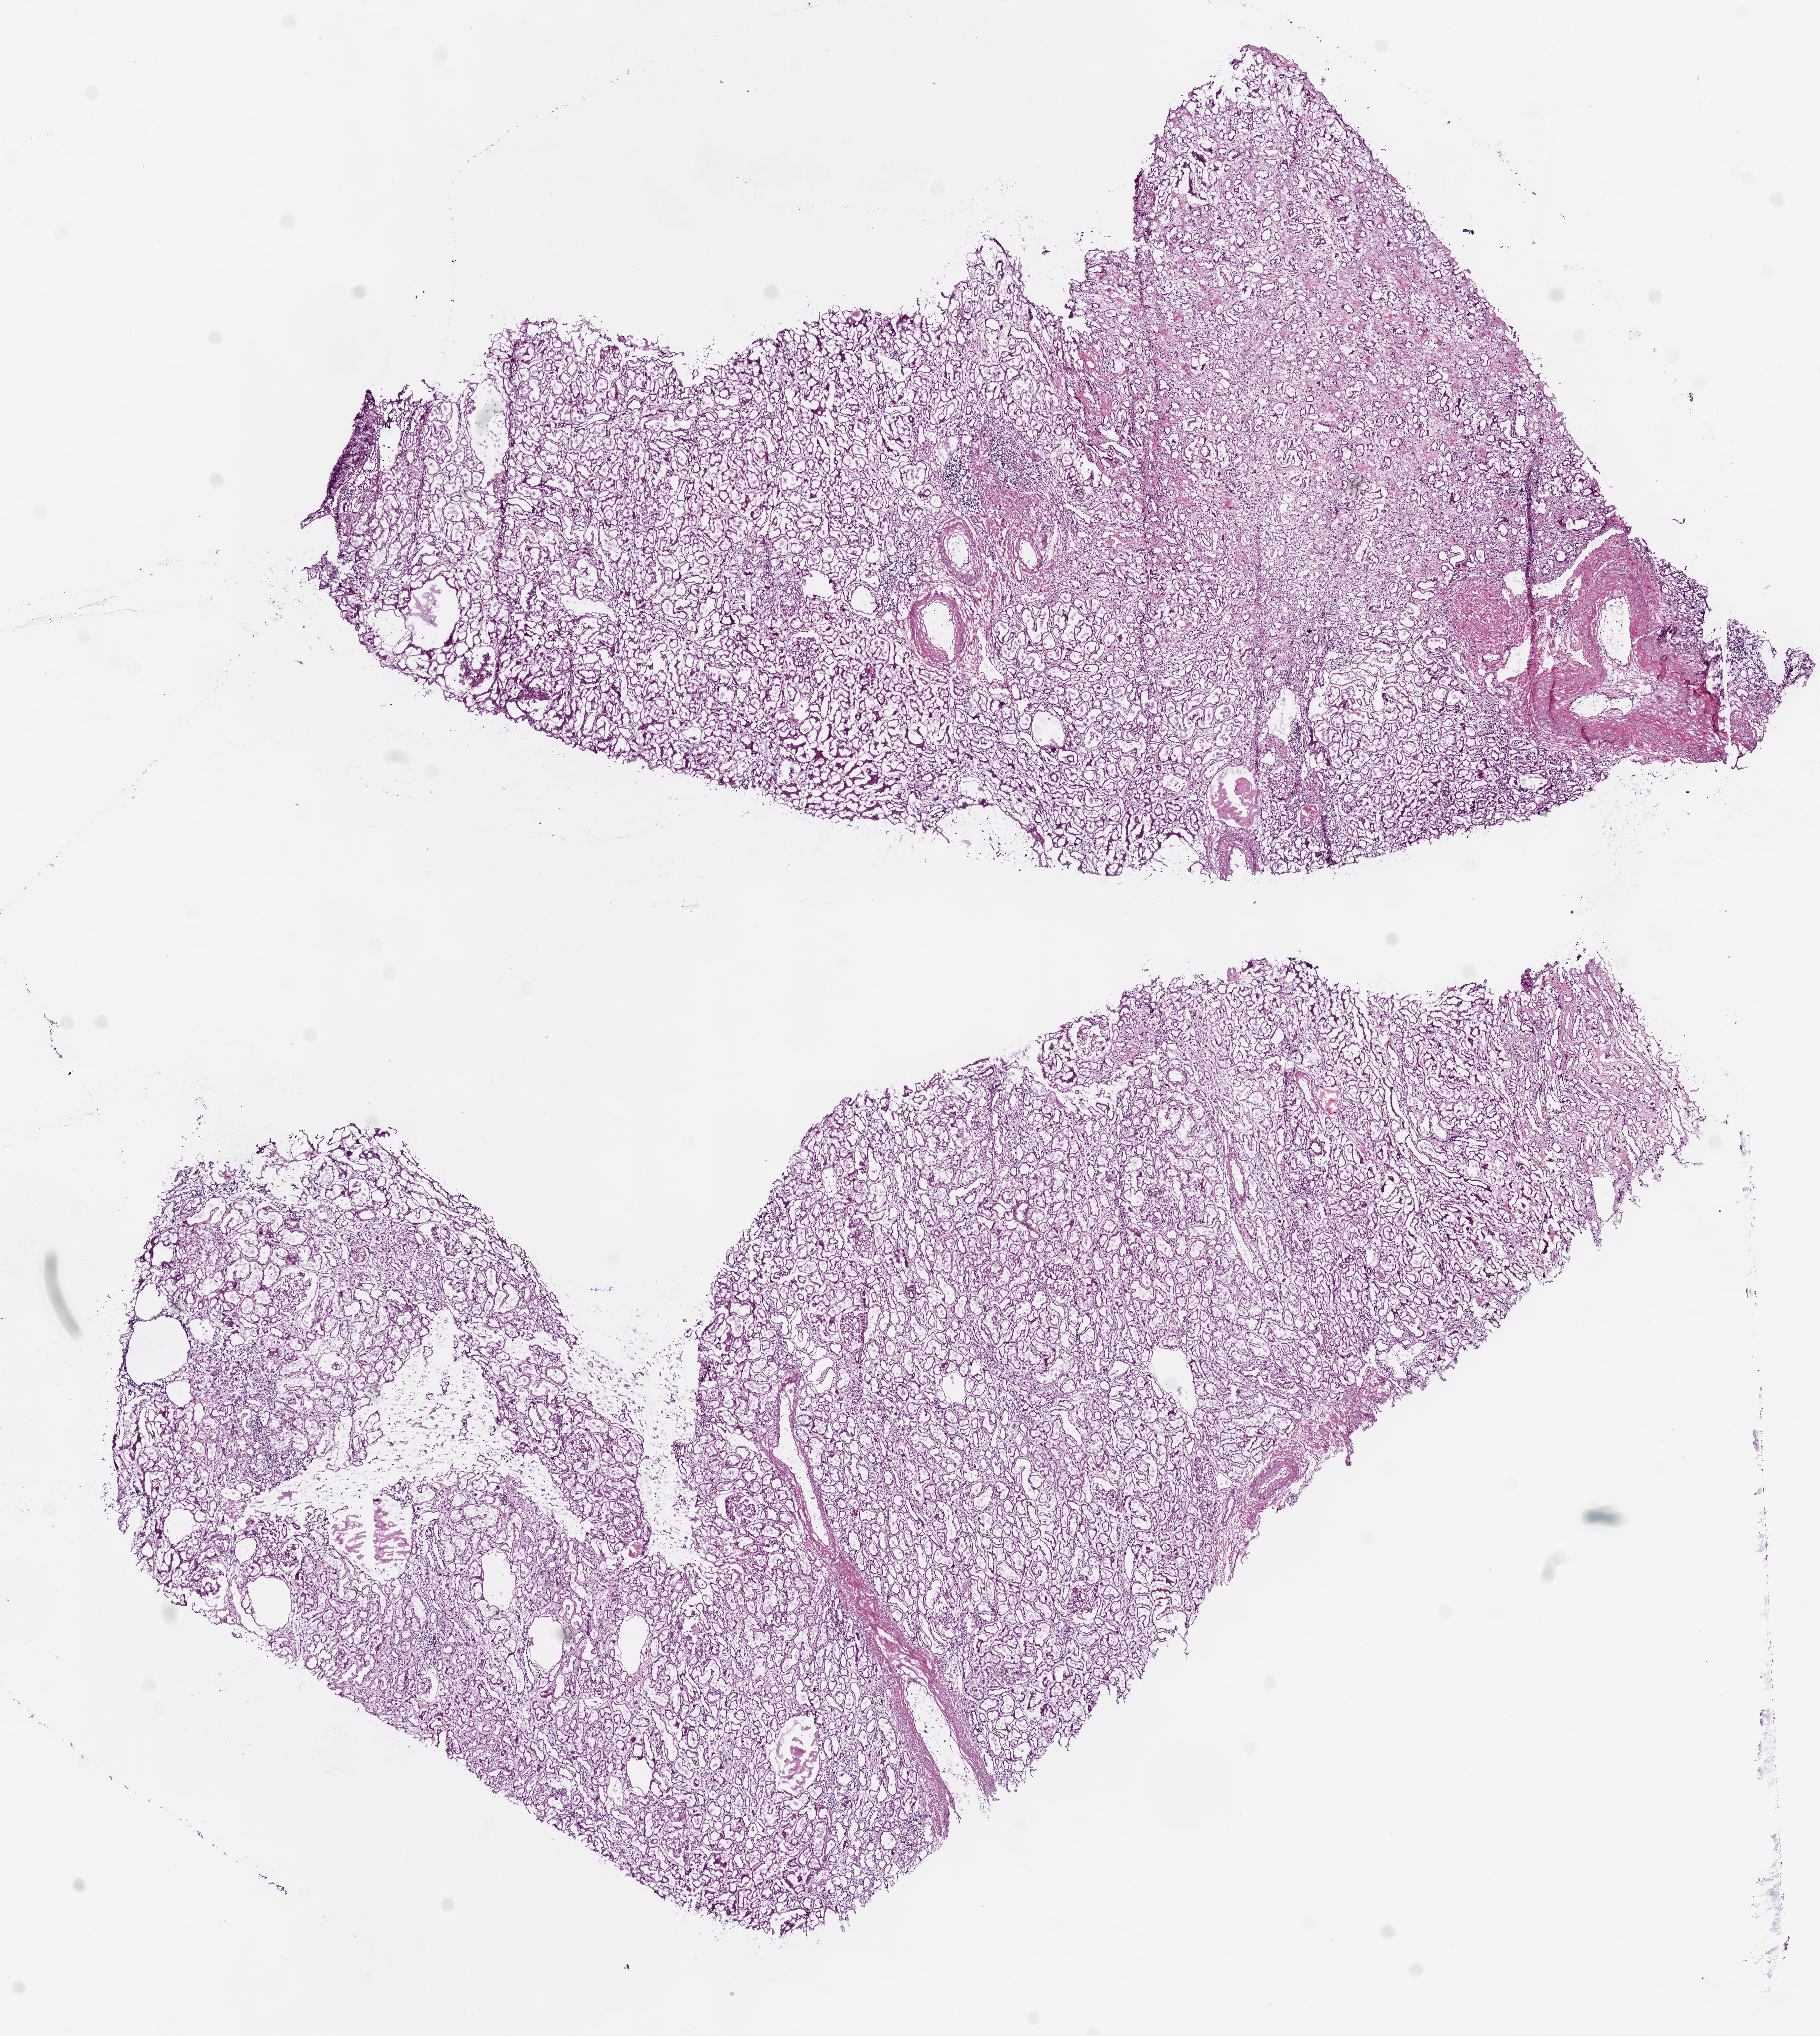
Digitized H&E tissue section (whole slide) — shown as a low-resolution overview of the whole scanned area (about 11.1 x 12.4 mm, acquisition: 20x scan). Frozen section from the top of the tissue portion. Sample: solid tissue normal (non-tumour tissue), kidney. Male patient.
This section: solid tissue normal (non-tumour) sample from the same patient. Patient diagnosis: Clear cell adenocarcinoma, NOS.